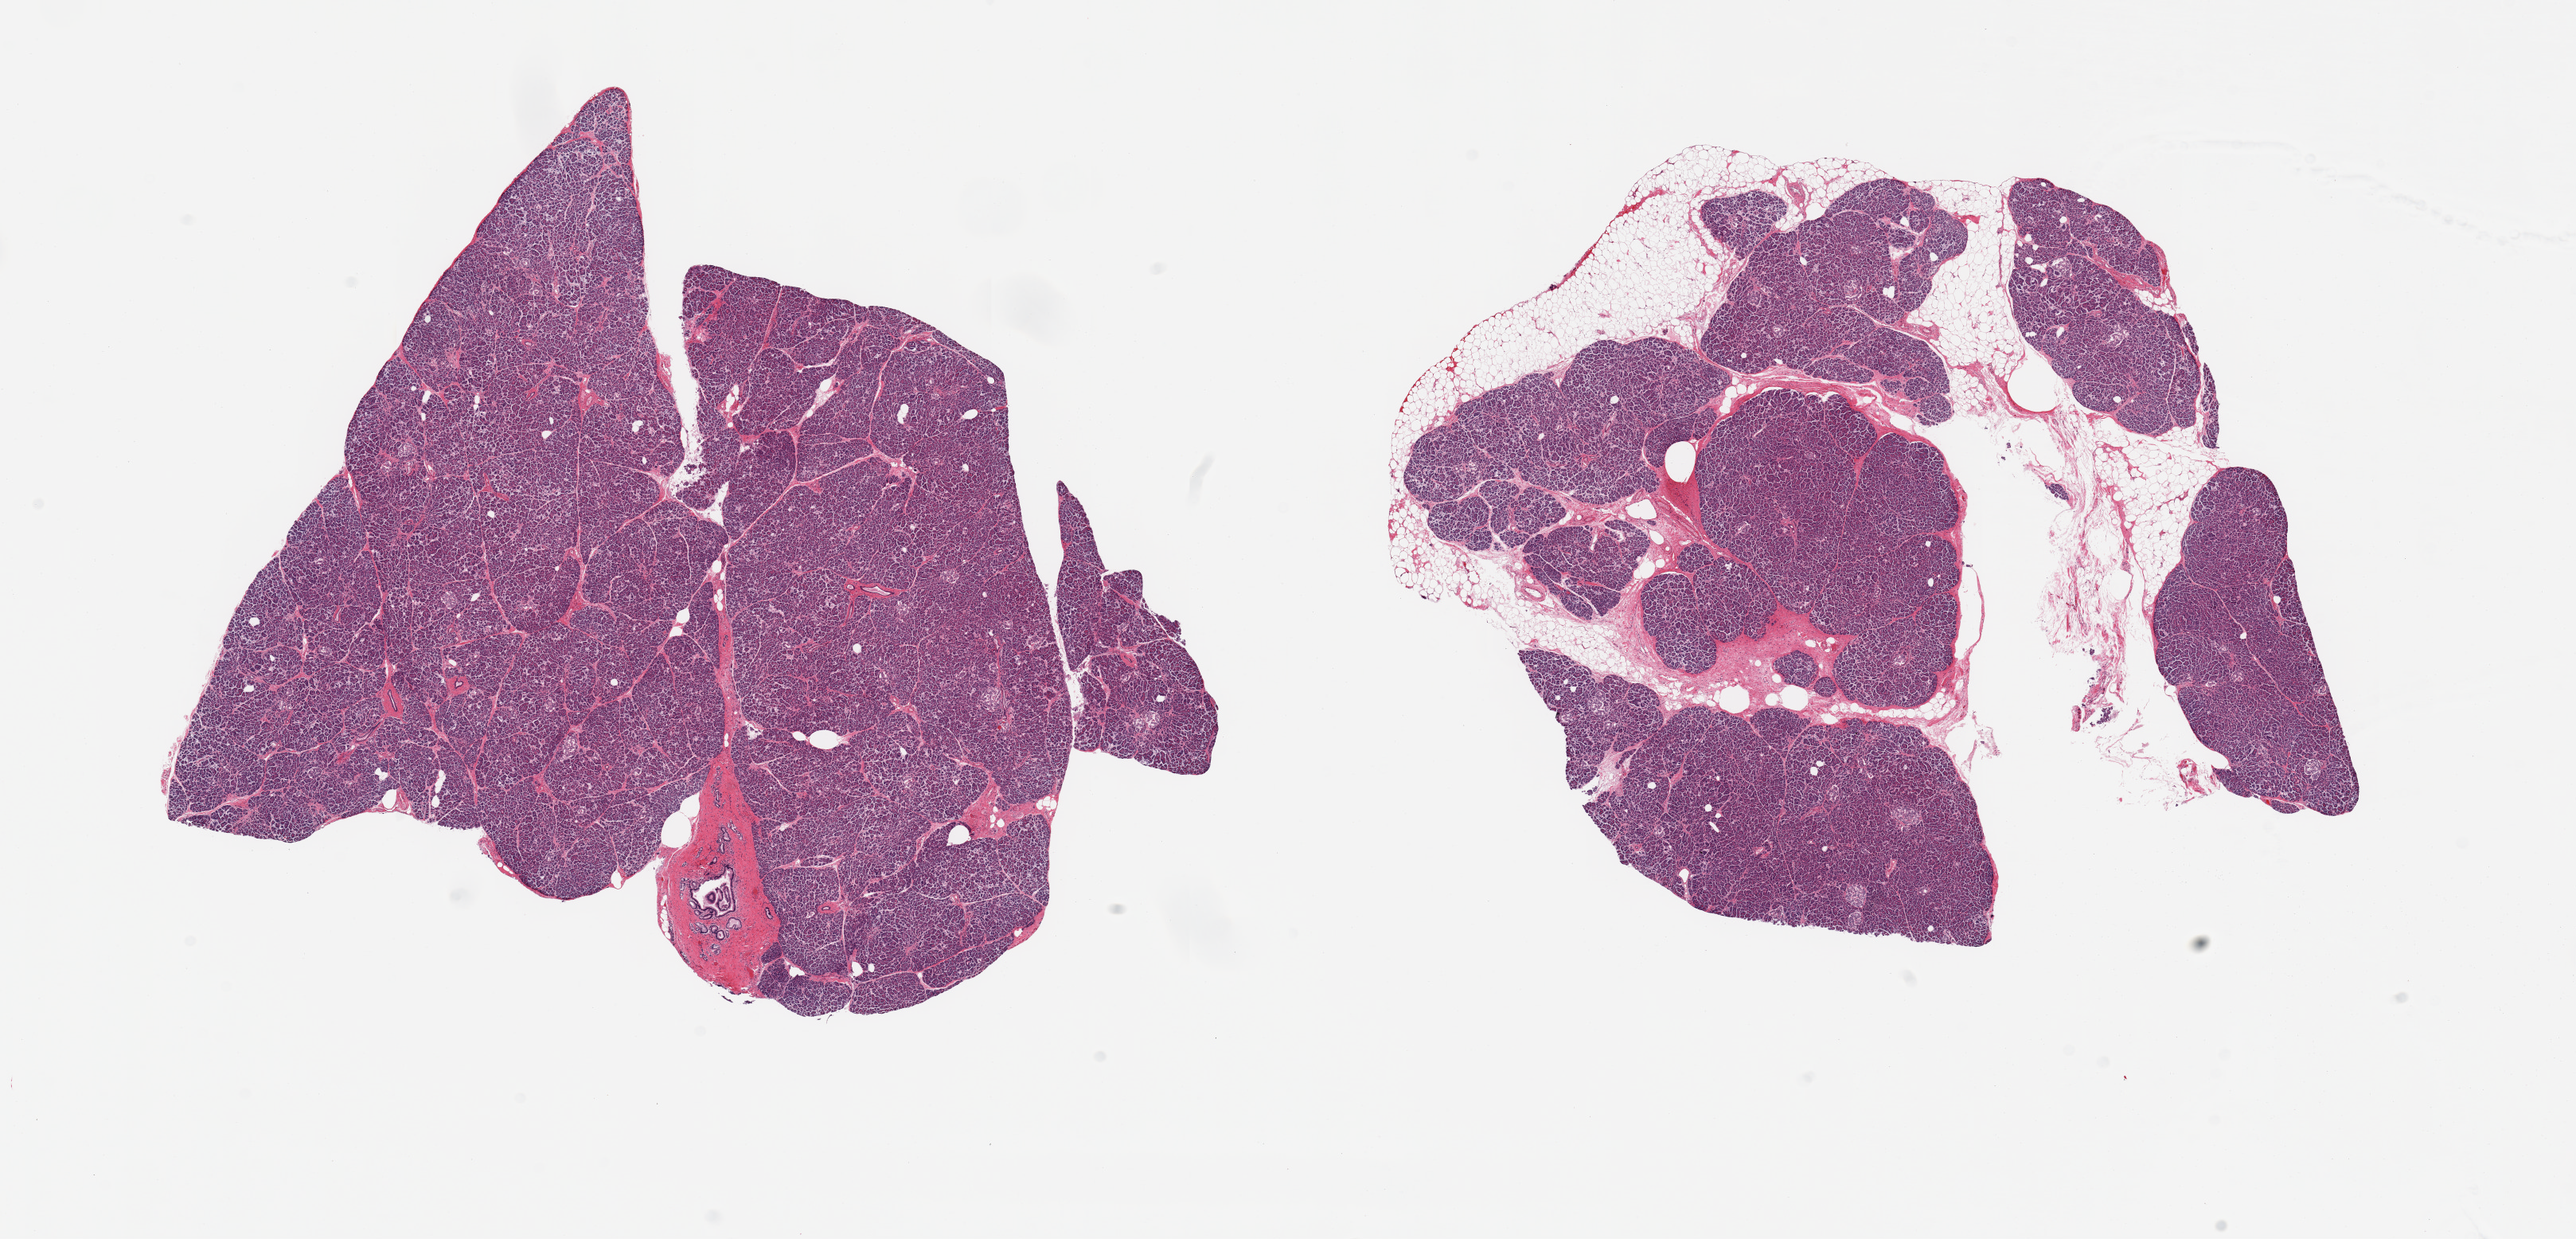
Hematoxylin and eosin (H&E) whole-slide image — whole scanned area (about 25.6 x 12.3 mm, acquisition: 20x scan) shown as a low-resolution overview; PAXgene-fixed, paraffin-embedded tissue; target tissue: pancreas; tissue donor sample. Donor: male.
Review note (as recorded): 2 pieces; one piece is ~25% fat (attached and internal), islets are well visualized.